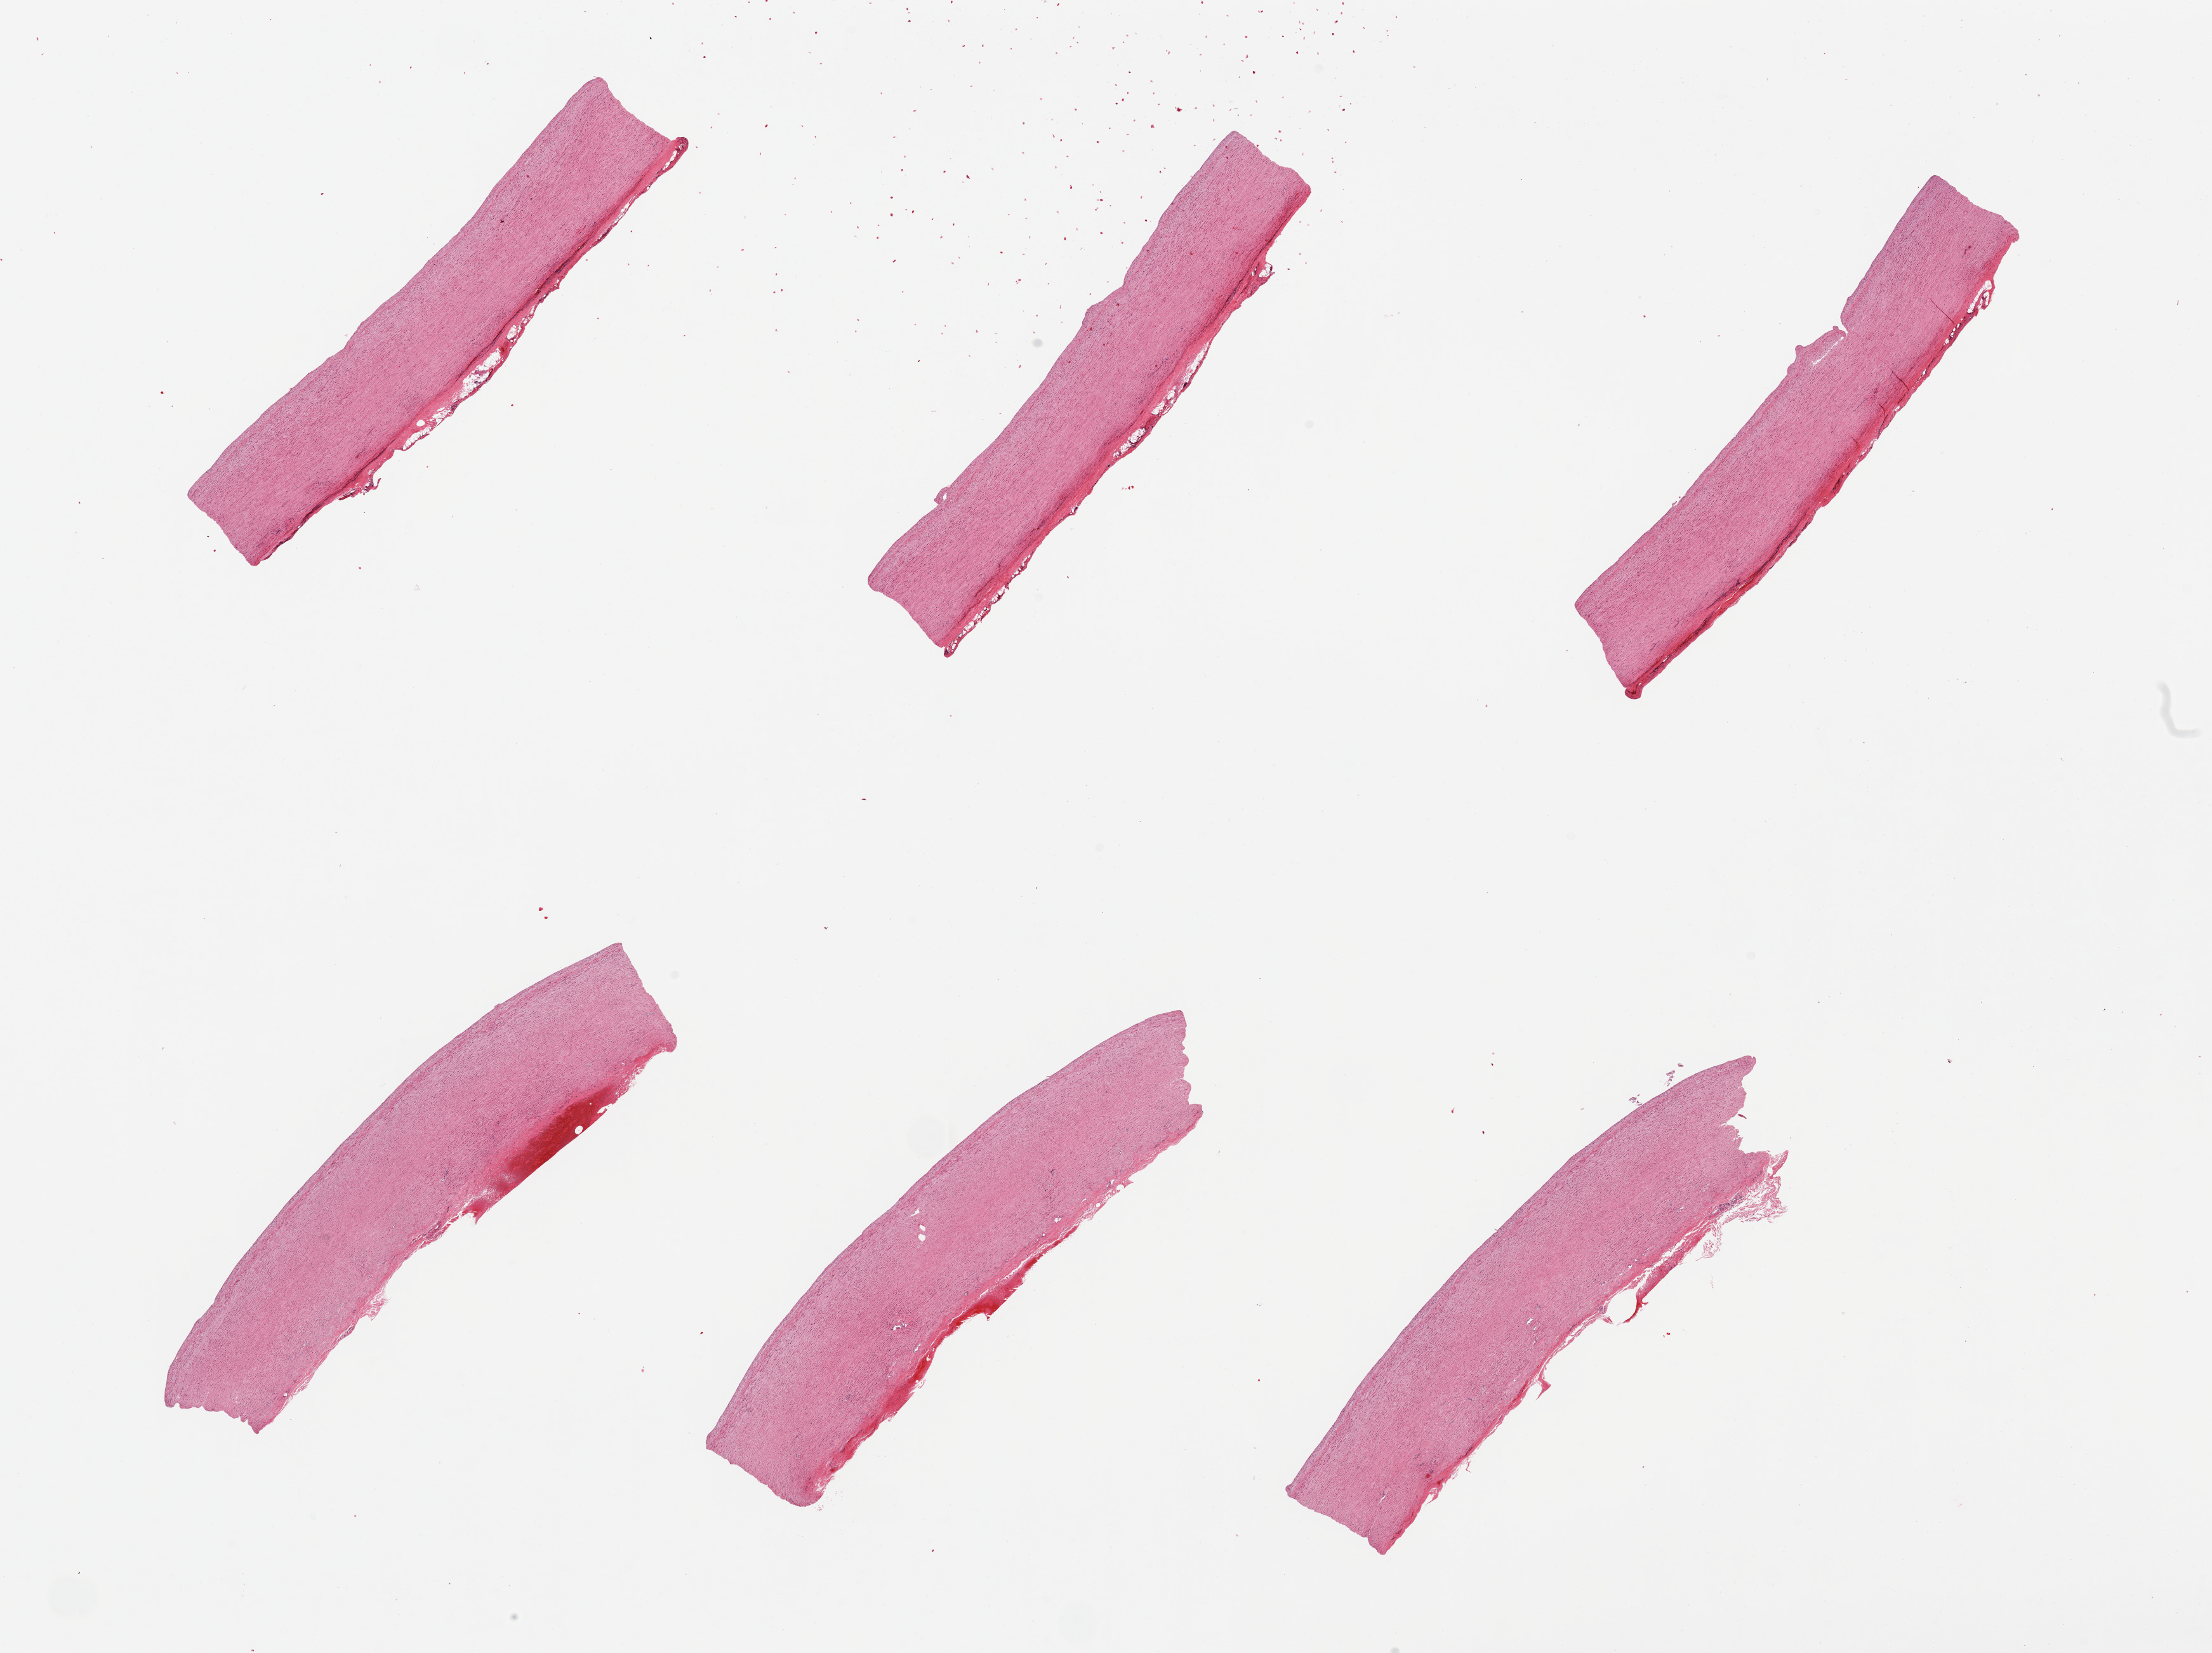
Digitized hematoxylin and eosin (H&E)-stained section — whole scanned area (about 27.6 x 20.6 mm) shown as a low-resolution overview, PAXgene-fixed paraffin-embedded (PFPE) section, section of aorta (target tissue), tissue donor sample.
• reviewer comment on this tissue sample: 6 pieces; minimal adherent serosa